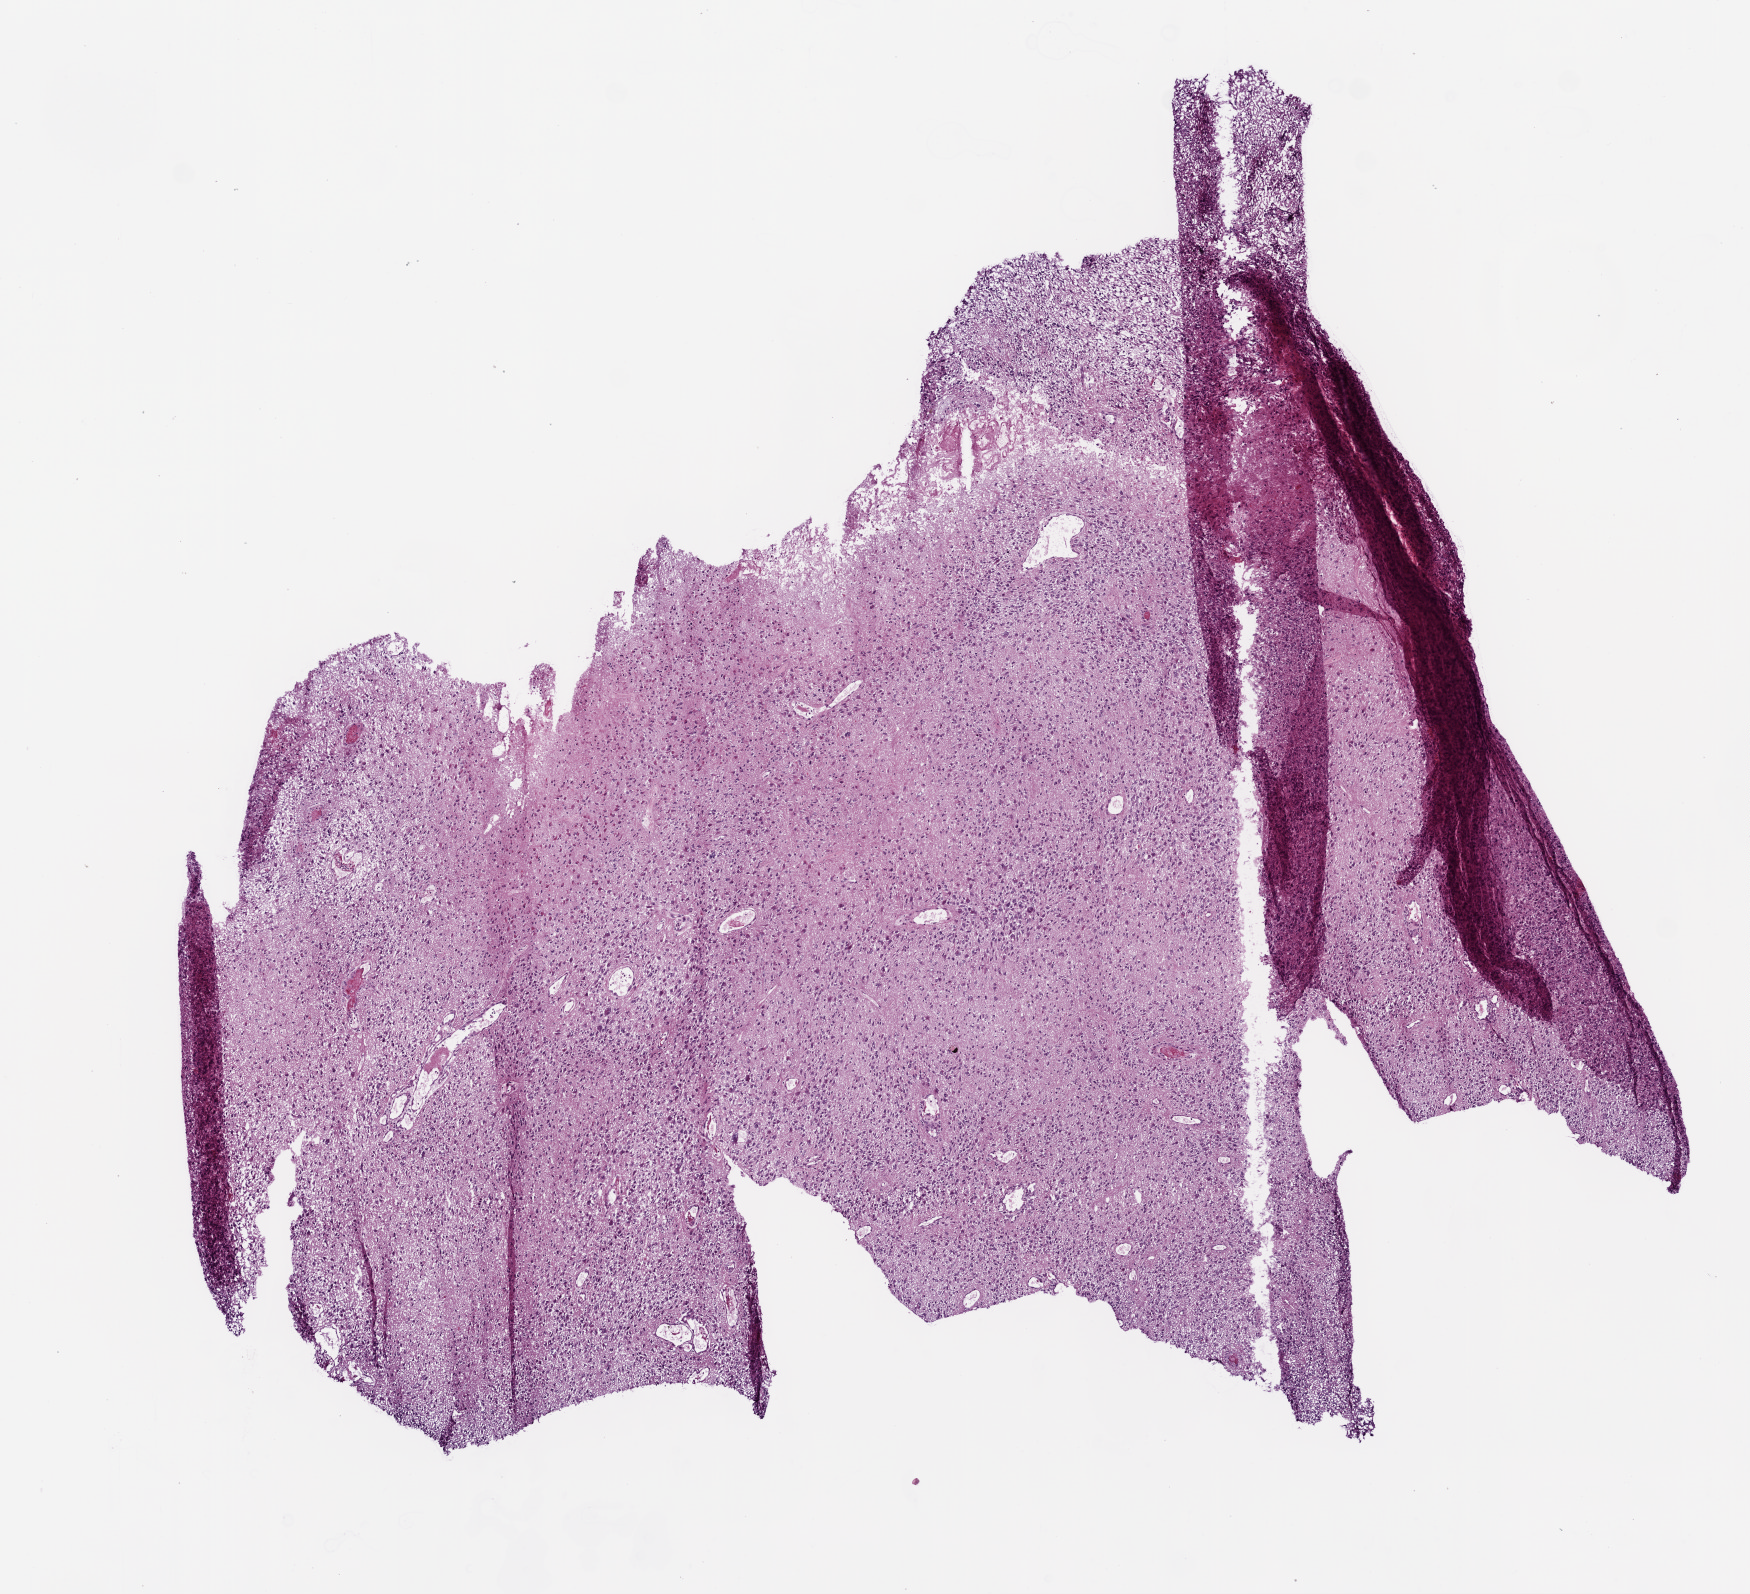
H&E whole-slide image — low-resolution overview of the scanned area, about 7.0 x 6.4 mm. Frozen section. Sample: primary tumour, brain. Male patient; age at initial diagnosis 73 years. Composition of this section per pathologist review: tumour cells 100%, tumour nuclei 80%, normal cells 0%, stromal cells 0%, necrosis 0%.
Histologic diagnosis: Glioblastoma.